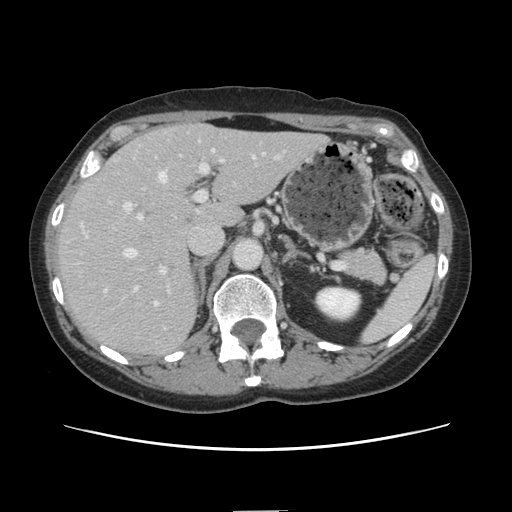
Contrast-enhanced abdominal CT, one axial slice. Slice 87 of 141 in the series (ordered by position). Soft-tissue window (W 400 / L 40 HU). 2.5 mm slice thickness. 512 × 512 image matrix, field of view 350 × 350 mm. Female patient, age 63 years. From the clinical record (not read from this slice): diagnosis: colorectal cancer liver metastases, imaged before liver resection; multiple liver metastases: yes; largest metastasis: 3.2 cm; disease in both lobes: yes.
Annotated regions visible in this slice (manually delineated by an expert):
- hepatic veins: box from (x=104, y=150) to (x=255, y=306) px
- liver: (x=58, y=124)–(x=326, y=356)
- planned liver remnant (the part of the liver to remain after resection): (x=177, y=125)–(x=326, y=227)
- portal vein (with intrahepatic branches): (x=122, y=153)–(x=264, y=294)
- liver metastasis: (x=169, y=265)–(x=175, y=272)